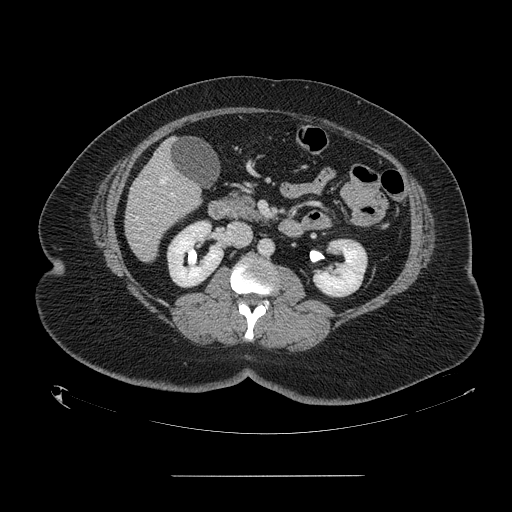
Contrast-enhanced abdominal CT, one axial slice; slice 57 of 164 in the series (ordered by position); intravenous contrast given; soft-tissue window (W 400 / L 40 HU); 512 × 512 image matrix, field of view 495 × 495 mm. Female patient, age 52 years. Case-level facts recorded for this patient, not image findings: diagnosis: colorectal cancer liver metastases, imaged before liver resection; multiple liver metastases: yes; largest metastasis: 3.5 cm; disease in both lobes: no.
Outlined on this slice (outlined manually by an expert reader):
- hepatic veins: bounding box <136,177,167,229> (left, top, right, bottom; pixels)
- liver: <125,144,202,262>
- portal vein (with intrahepatic branches): <170,193,174,197>